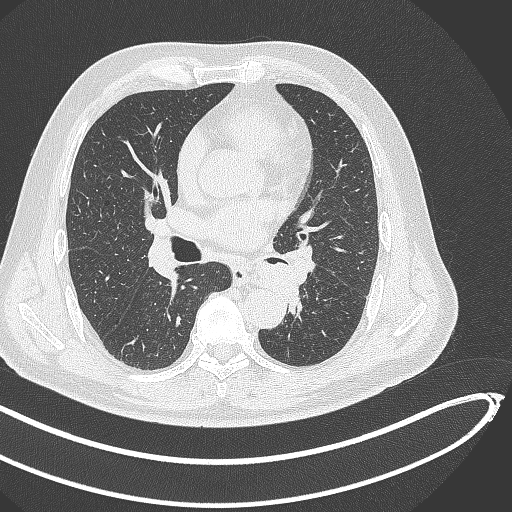
Chest CT, one axial slice. Position 251 of 468 along the scan axis. Reconstruction kernel B70f. 120 kVp. Lung window (W 1500 / L -600 HU). 512 × 512 image matrix, field of view 400 × 400 mm. Patient: male, 64 years. Case-level facts recorded for this patient, not image findings: clinical TNM (as recorded): T1c N0 M0.
Outlined on this slice (bounding box drawn by a radiologist):
- lung tumour (recorded histology: squamous cell carcinoma): bounding box [x1, y1, x2, y2] px = [251, 261, 307, 306]